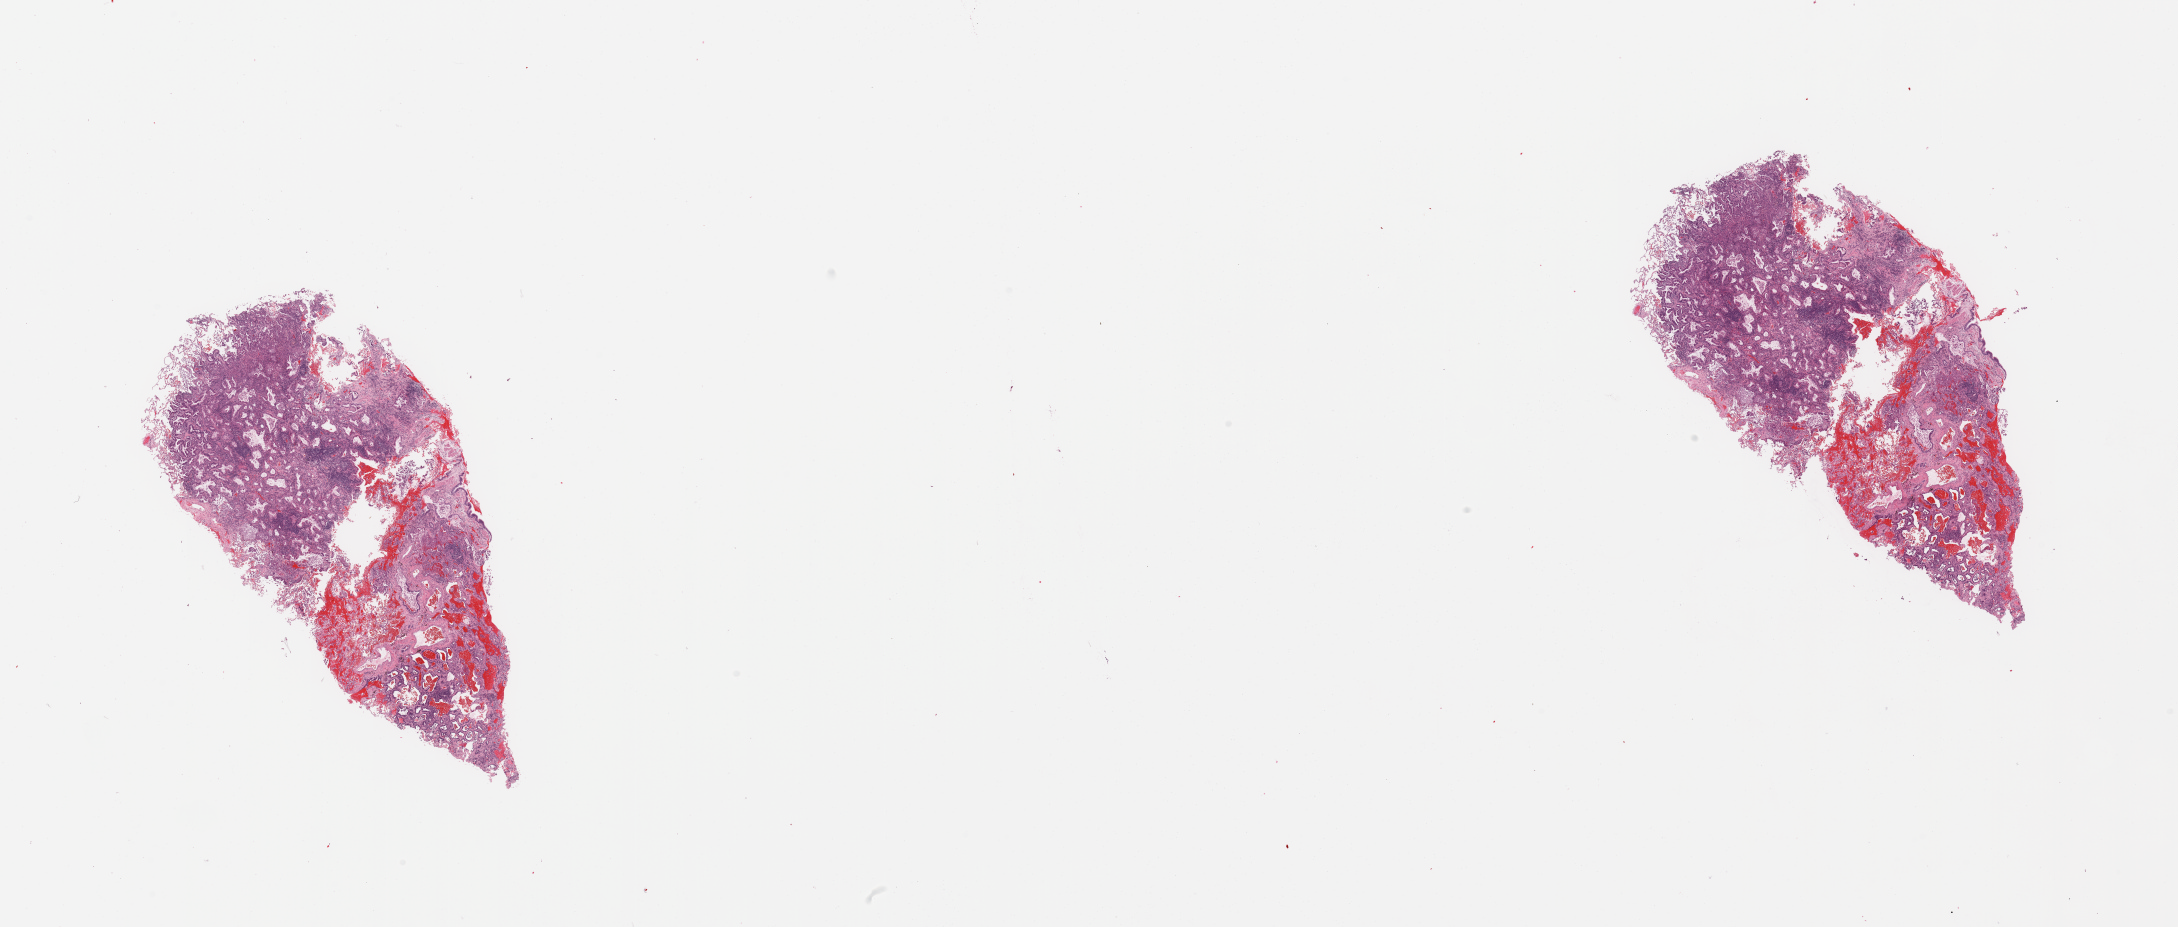
H&E-stained whole-slide image, shown as a low-resolution overview of the whole scanned area (about 34.5 x 14.7 mm); tumour tissue sample, sampled site: lung. Male, 69 y/o. Histologic grade: G2 (moderately differentiated). Composition of this section per pathologist review: tumour nuclei 70%, necrosis 5%.
Diagnosis: Adenocarcinoma, NOS. Primary tumour site (as recorded): right upper lobe. AJCC pathologic stage: IA.